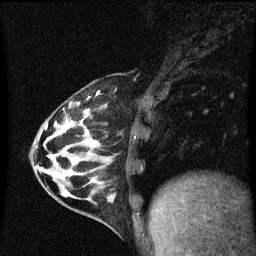
Breast MRI (dynamic contrast-enhanced), one sagittal slice. Slice 21 of 60 in the series (ordered by position). Dynamic contrast-enhanced series, image 2 of 3 at this slice position (ordered by acquisition). 1.5 T. TE 4.2 ms, TR 8.4 ms. 2 mm slice thickness. 256 × 256 image matrix. Patient: female, 32 years.
Annotated regions visible in this slice (semi-automatic segmentation, software-assisted and operator-edited):
- analysis volume of interest (the breast-tissue region the enhancement analysis was run in; not a lesion): box from (x=34, y=82) to (x=151, y=169) px
- tumour enhancement mask (voxels above the 70 % enhancement threshold inside the analysis volume of interest): (x=45, y=92)–(x=100, y=129)